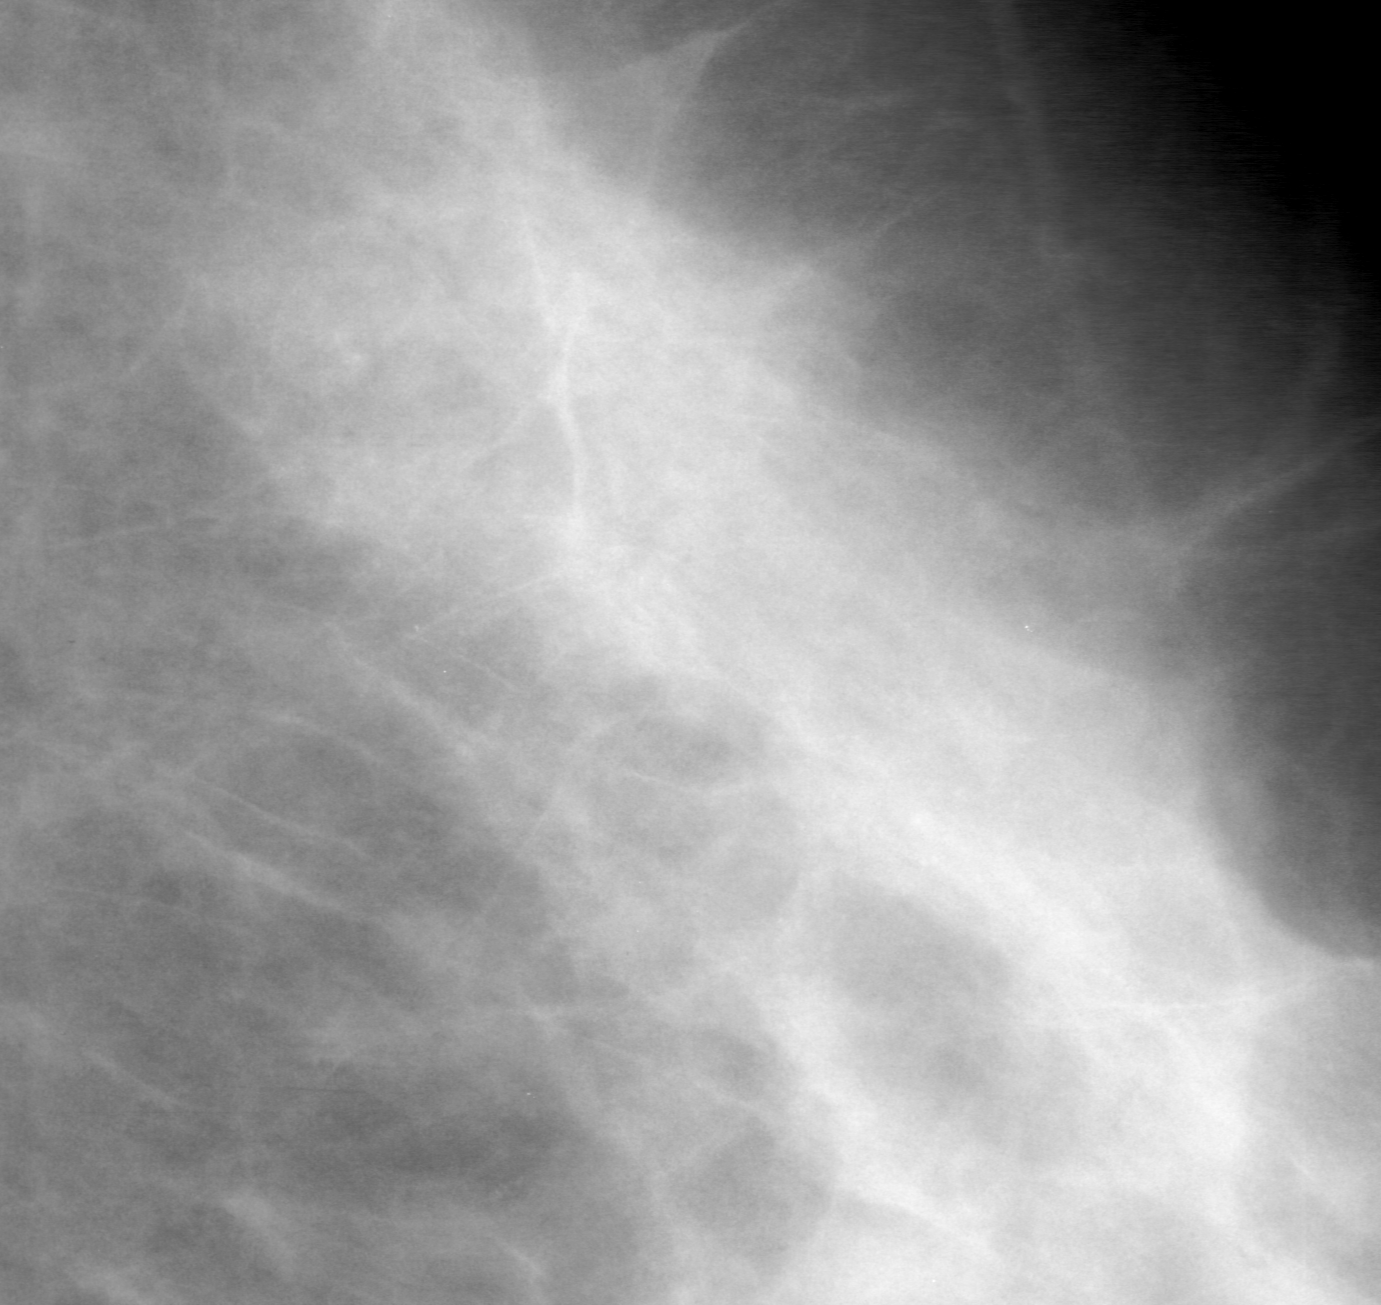
Crop from a digitized film mammogram around one marked abnormality, left breast, CC view, BI-RADS breast density category 3 (scale 1–4).
Marked abnormality: calcifications, morphology amorphous, distribution segmental; BI-RADS assessment category 0; pathology result (as recorded, not read from the image): benign.